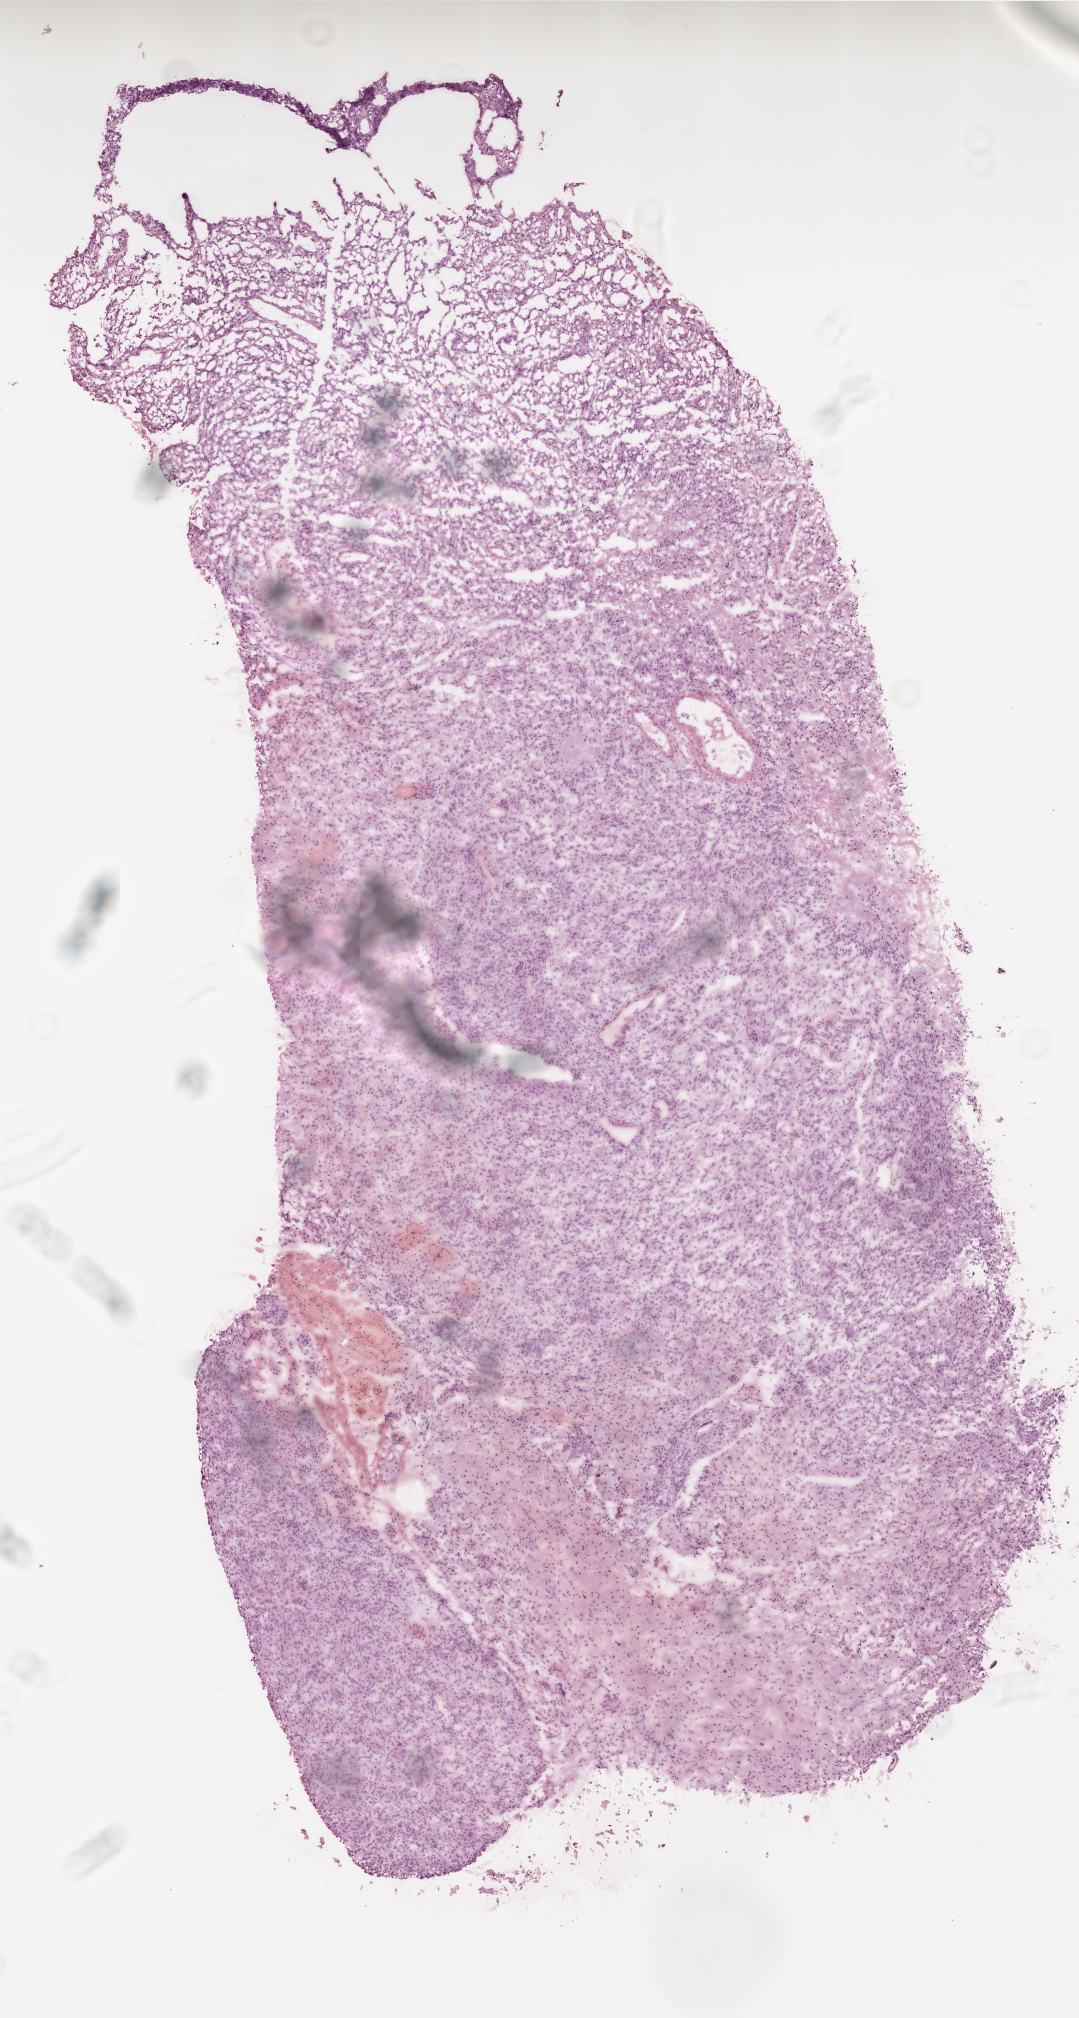
Digitized H&E-stained tissue section (whole slide) — whole scanned area (about 4.3 x 8.1 mm) shown as a low-resolution overview. Frozen section from the top of the tissue portion. Brain, primary tumour sample. Female patient; age at initial diagnosis 48 years. Slide review estimates, as recorded: tumour cells 80%, tumour nuclei 95%, normal cells 0%, stromal cells 10%, necrosis 10%.
Histologic diagnosis: Glioblastoma.